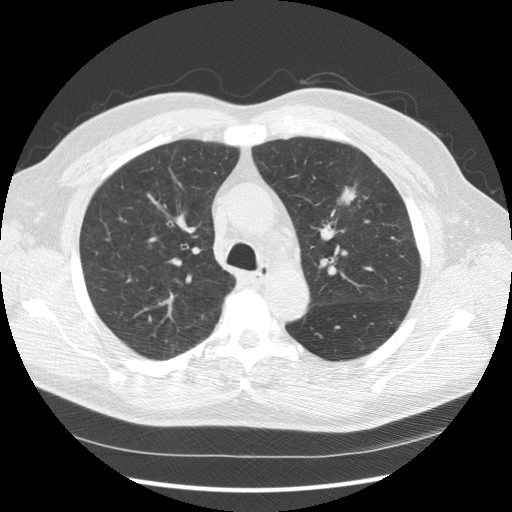
Low-dose screening chest CT, one axial slice. Position 109 of 157 along the scan axis. Reconstruction kernel STANDARD. Lung window (W 1500 / L -600 HU). 2.5 mm slice thickness. 512 × 512 image matrix, field of view 370 × 370 mm.
Outlined on this slice (outlined manually by an expert reader):
- lesion 1 (tumor, upper lobe of left lung): box from (x=339, y=187) to (x=356, y=205) px